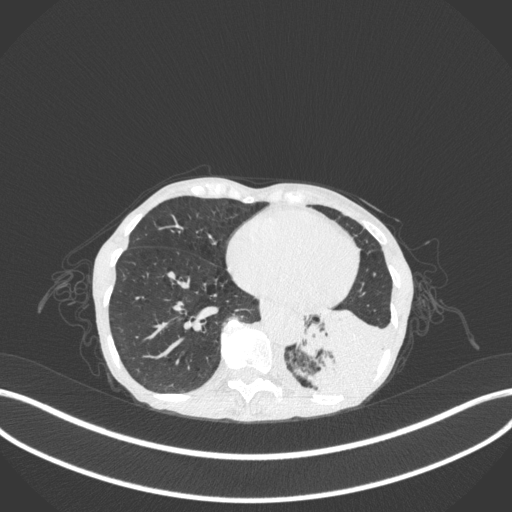
Chest CT, one axial slice. Reconstruction kernel B31f. Lung window (W 1500 / L -600 HU). 512 × 512 image matrix. Patient: female, 70 years. Case-level facts recorded for this patient, not image findings: clinical TNM (as recorded): T3 N0 M0.
Annotated regions visible in this slice (bounding box drawn by a radiologist):
- lung tumour (recorded histology: small cell carcinoma): bounding box [x1, y1, x2, y2] px = [303, 304, 394, 403]